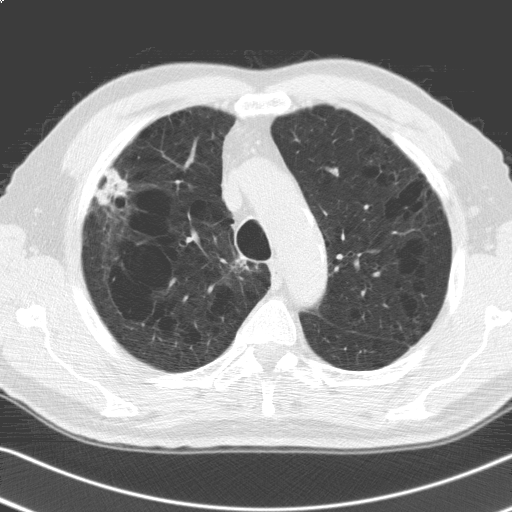
Chest CT (low-dose screening protocol), one axial image, second screening round (one year after baseline), lung window (W 1500 / L -600 HU), 3.2 mm slice thickness, slice 38 of 168 in the series. Male participant, aged 69 years at enrolment. Former smoker at enrolment.
• Expert reader's lesion annotation, box from (x=88, y=166) to (x=133, y=218) px.
• The screening reader recorded 6 non-calcified nodules or masses ≥4 mm on this exam (right upper lobe, right upper lobe, right lower lobe, lingula, left lower lobe, left lower lobe); which of them this box marks is not recorded.
• Participant outcome: lung cancer diagnosed 91 days after this screen — adenosquamous carcinoma, right upper lobe, poorly differentiated (G3), stage IV (AJCC 6th edition), 30 mm at pathology.